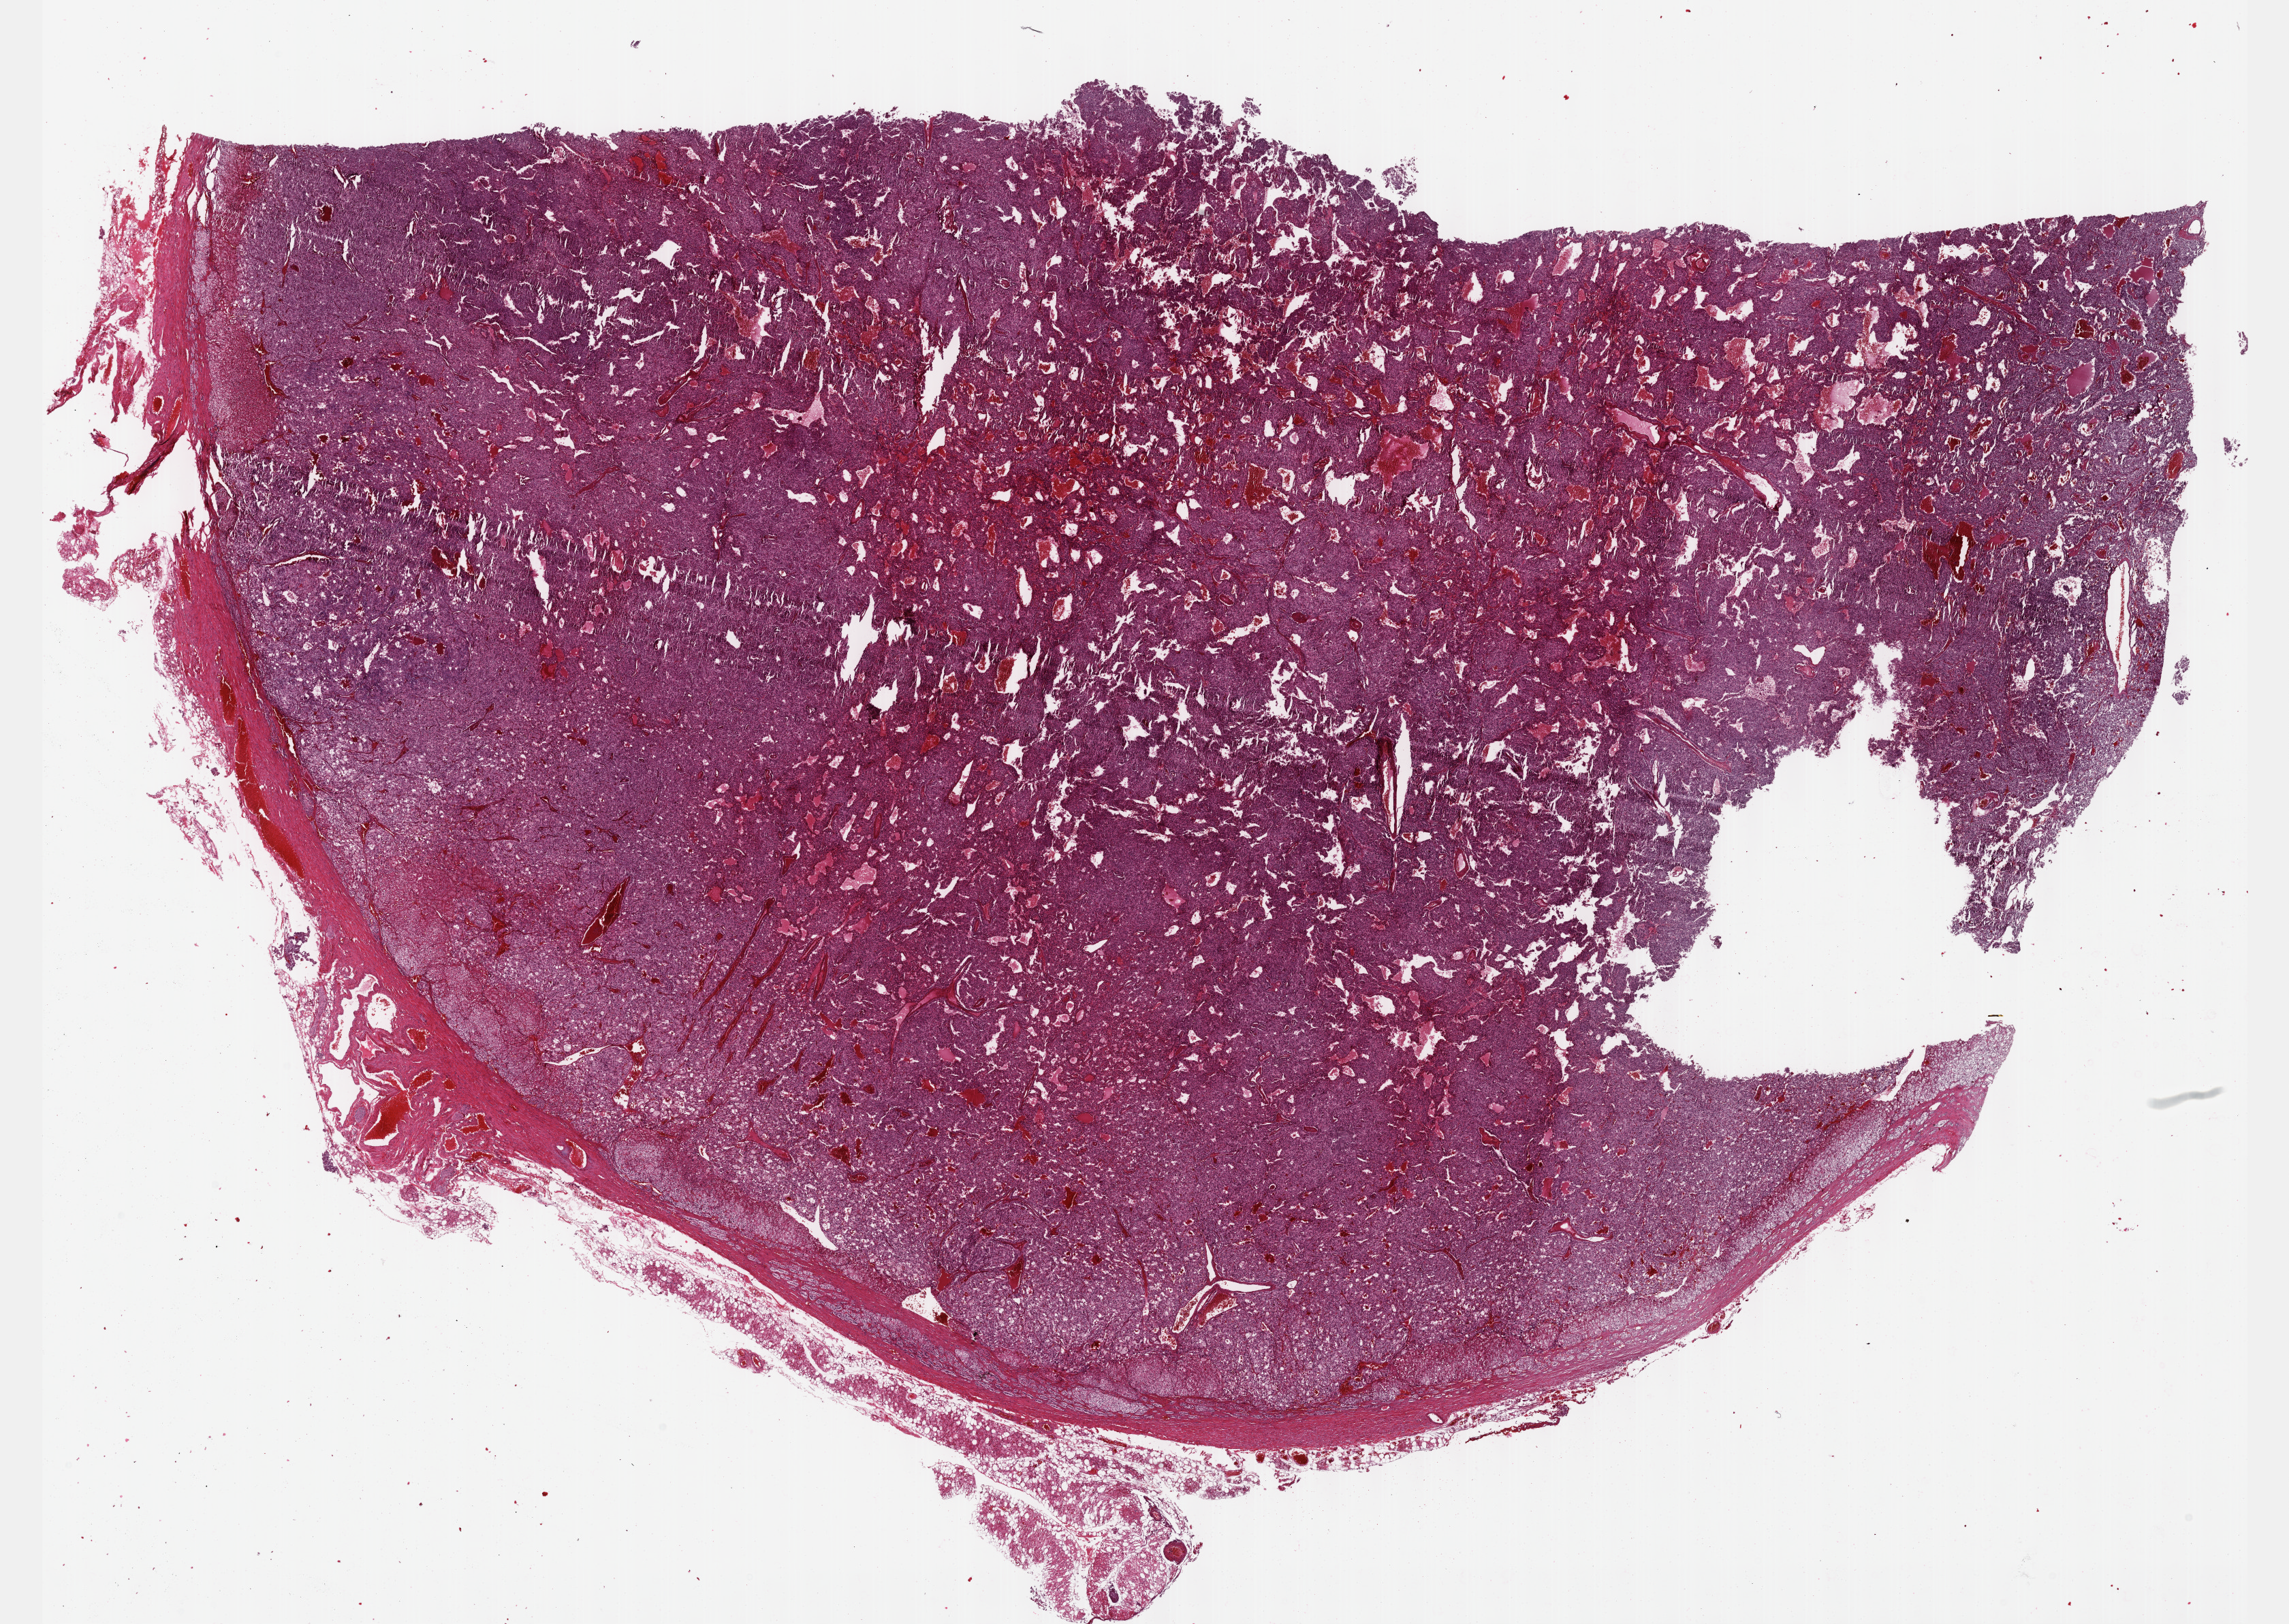
Digitized H&E tissue section (whole slide), low-resolution overview of the scanned area, about 27.2 x 19.3 mm. Formalin-fixed paraffin-embedded (FFPE) diagnostic section. Primary tumour sample from the adrenal gland. Patient: female, age at initial diagnosis 42 years.
Histologic diagnosis: Pheochromocytoma, NOS.